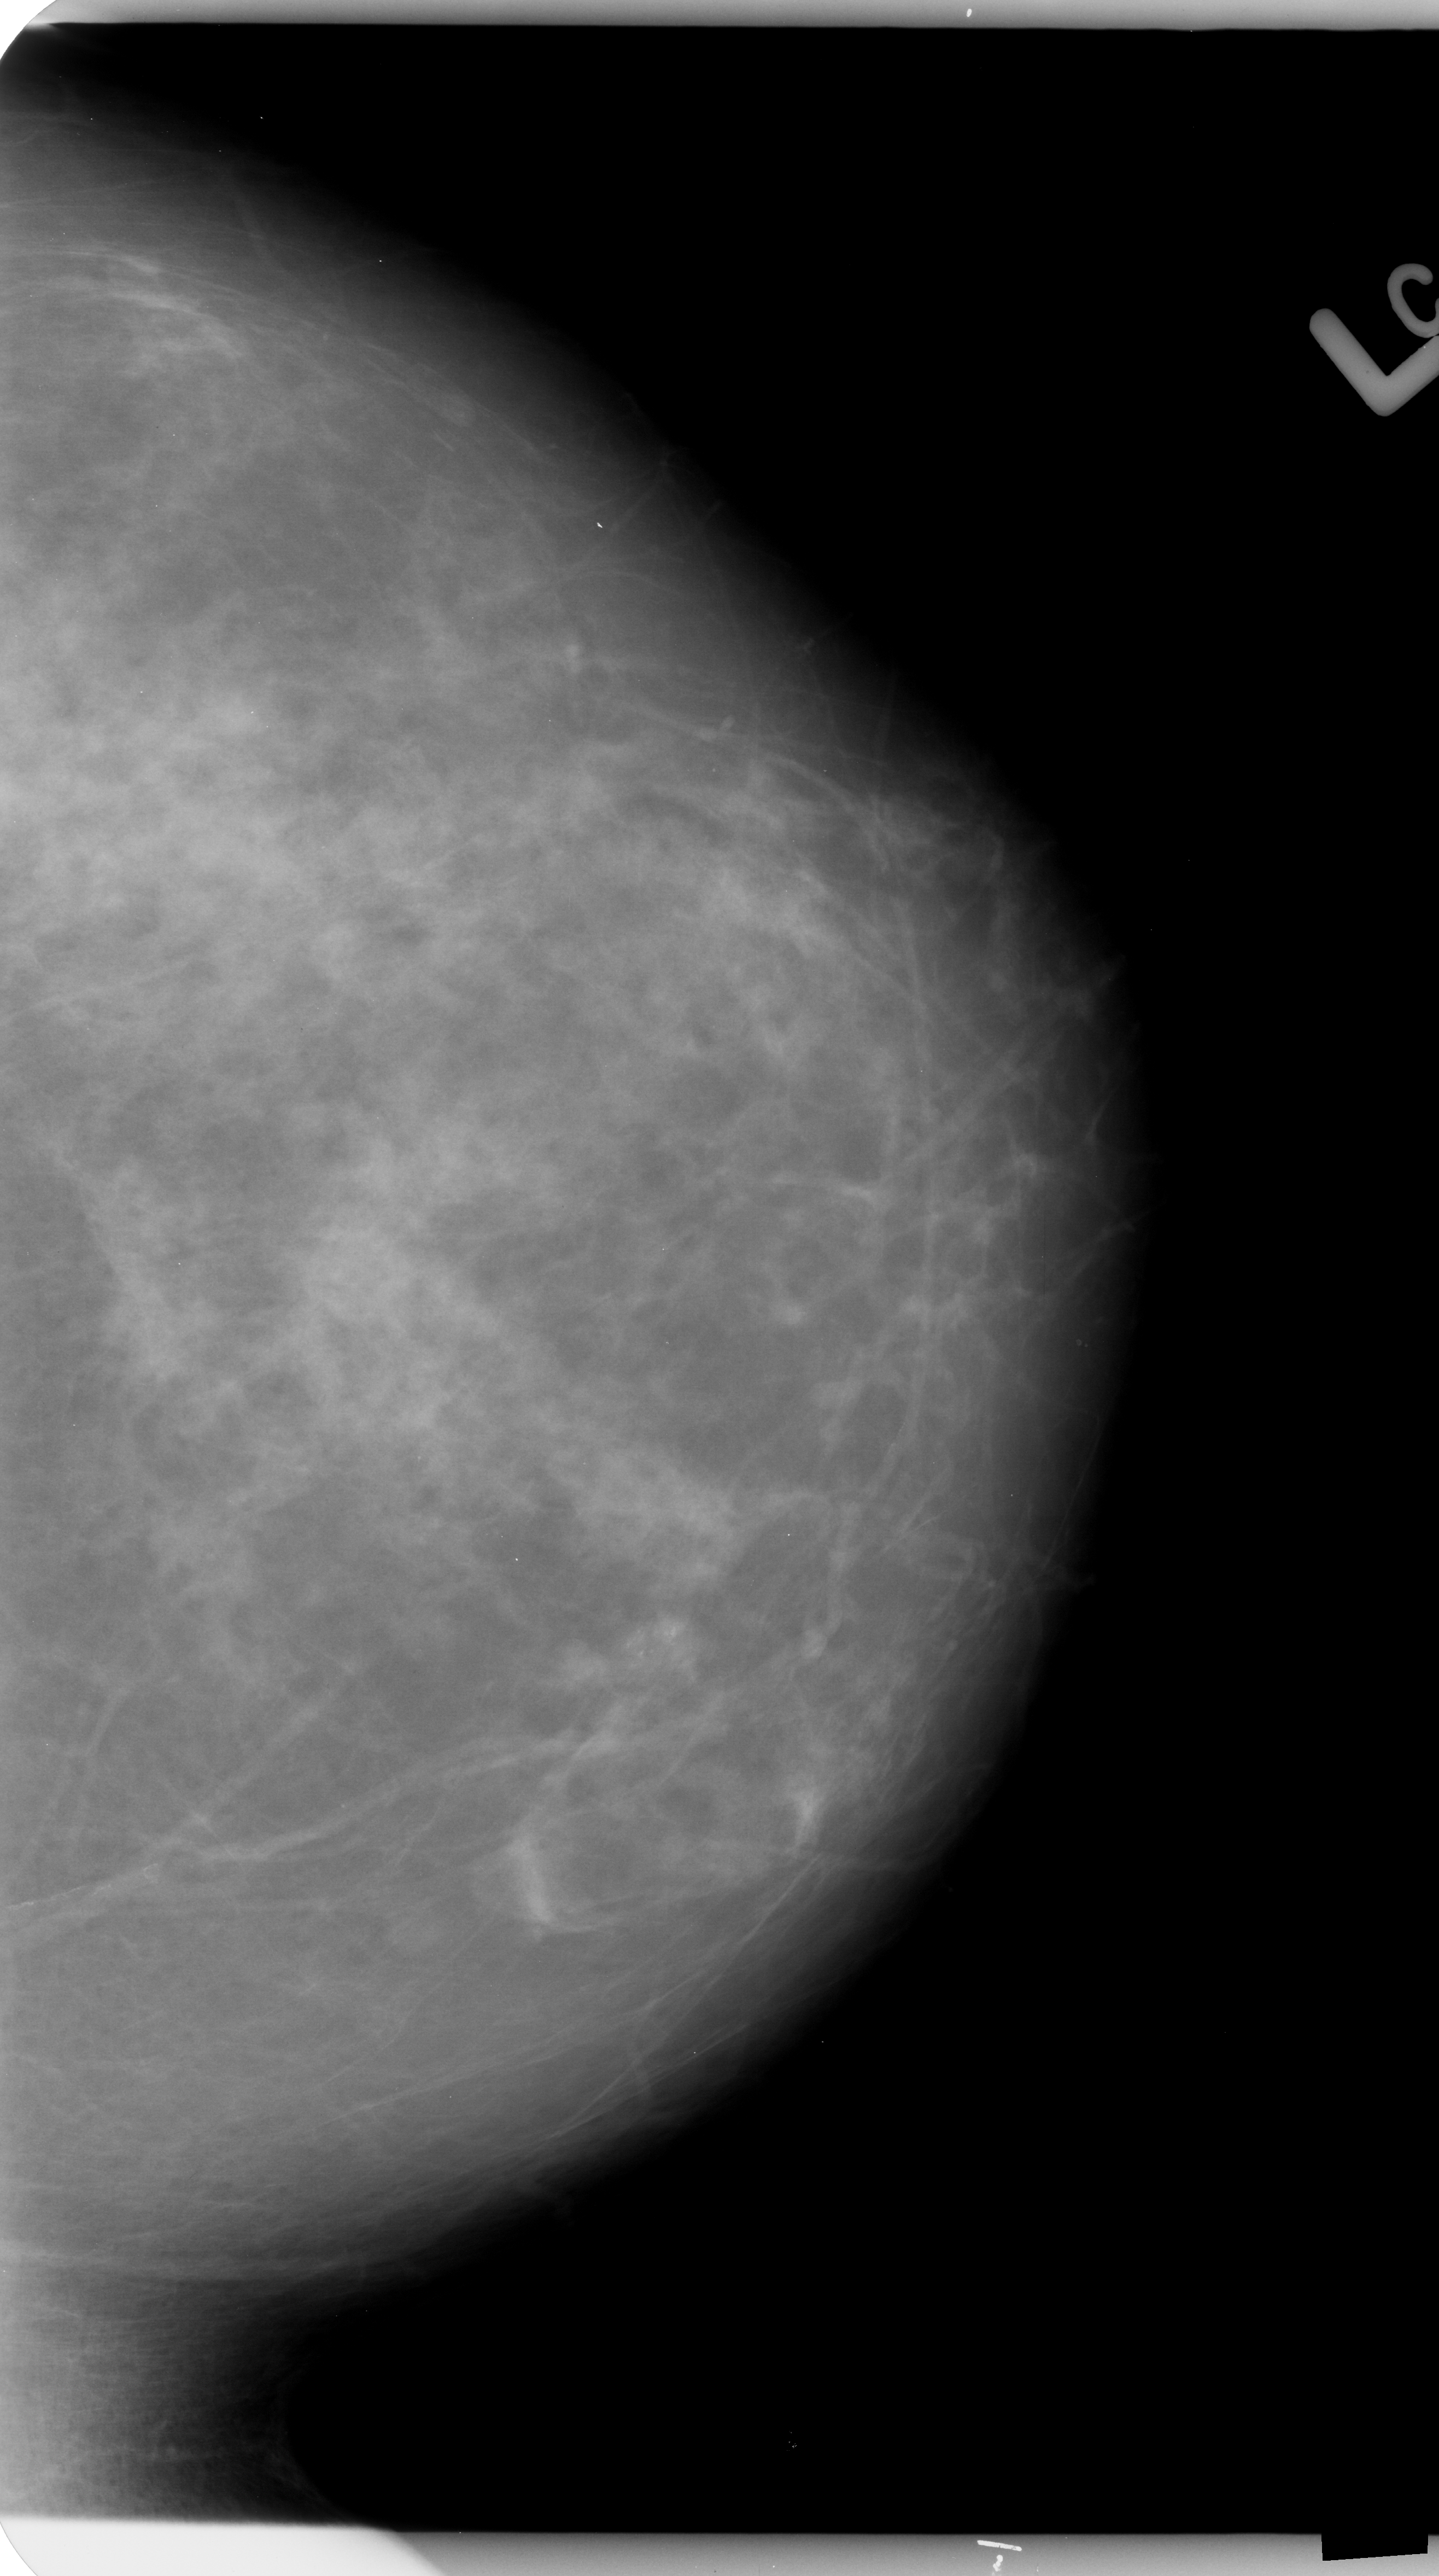
Mammogram (digitized film); left breast; craniocaudal (CC) view; breast composition: scattered fibroglandular densities (BI-RADS density category 2 of 4); 1439 × 2576 image matrix.
Expert-marked regions of interest on this film, with their recorded descriptors:
- calcifications, morphology pleomorphic, distribution clustered; BI-RADS assessment category 4; pathology result (as recorded, not read from the image): benign: bounding box (x1, y1, x2, y2) in pixels: (533, 1556, 745, 1720)